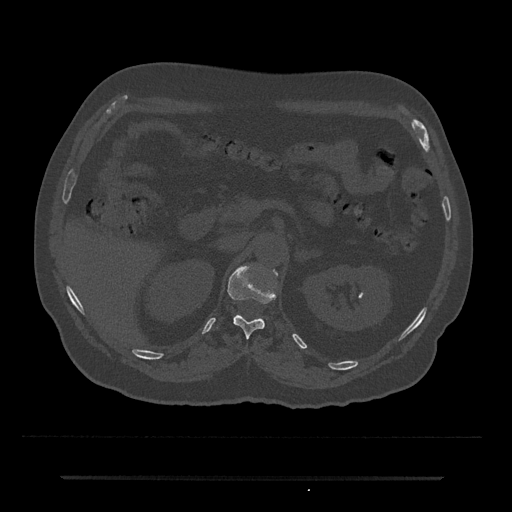
CT including the spine, one axial slice. Slice 118 of 797 in the series (ordered by position). Reconstruction kernel Br40s/3. Bone window (W 1800 / L 400 HU). 0.5 mm slice thickness. 512 × 512 image matrix, field of view 437 × 437 mm. Male patient, age 69 years. Case-level facts recorded for this patient, not image findings: primary cancer: prostate.
Structures marked on this image (semi-automatically segmented with operator editing):
- T12 vertebra: bounding box [x1, y1, x2, y2] px = [216, 264, 277, 338]